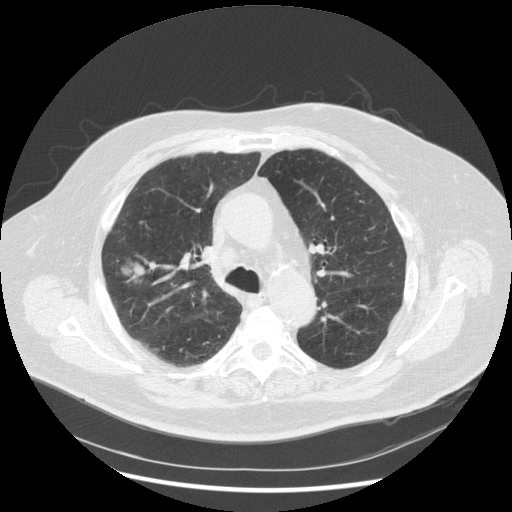
Low-dose screening chest CT, one axial slice; position 188 of 263 along the scan axis; reconstruction kernel STANDARD; 120 kVp; lung window (W 1500 / L -600 HU); 2.5 mm slice thickness; 512 × 512 image matrix, field of view 400 × 400 mm.
Outlined on this slice (manually delineated by an expert):
- lesion 1 (tumor, upper lobe of right lung): bounding box [x1, y1, x2, y2] px = [121, 262, 145, 282]